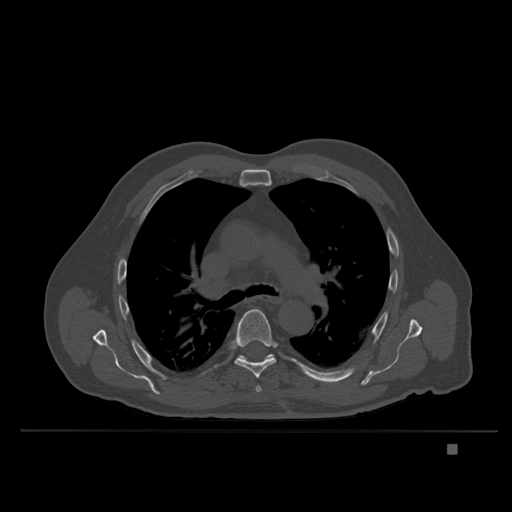
CT including the spine, one axial slice; slice 258 of 435 in the series (ordered by position); bone window (W 1800 / L 400 HU); 1.5 mm slice thickness; 512 × 512 image matrix, field of view 434 × 434 mm. Male patient, age 73 years. From the clinical record (not read from this slice): primary cancer: skin.
Annotated regions visible in this slice (semi-automatically segmented with operator editing):
- T5 vertebra: bounding box [x1, y1, x2, y2] px = [256, 386, 262, 392]
- T6 vertebra: [230, 309, 277, 379]
- T7 vertebra: [235, 354, 275, 363]